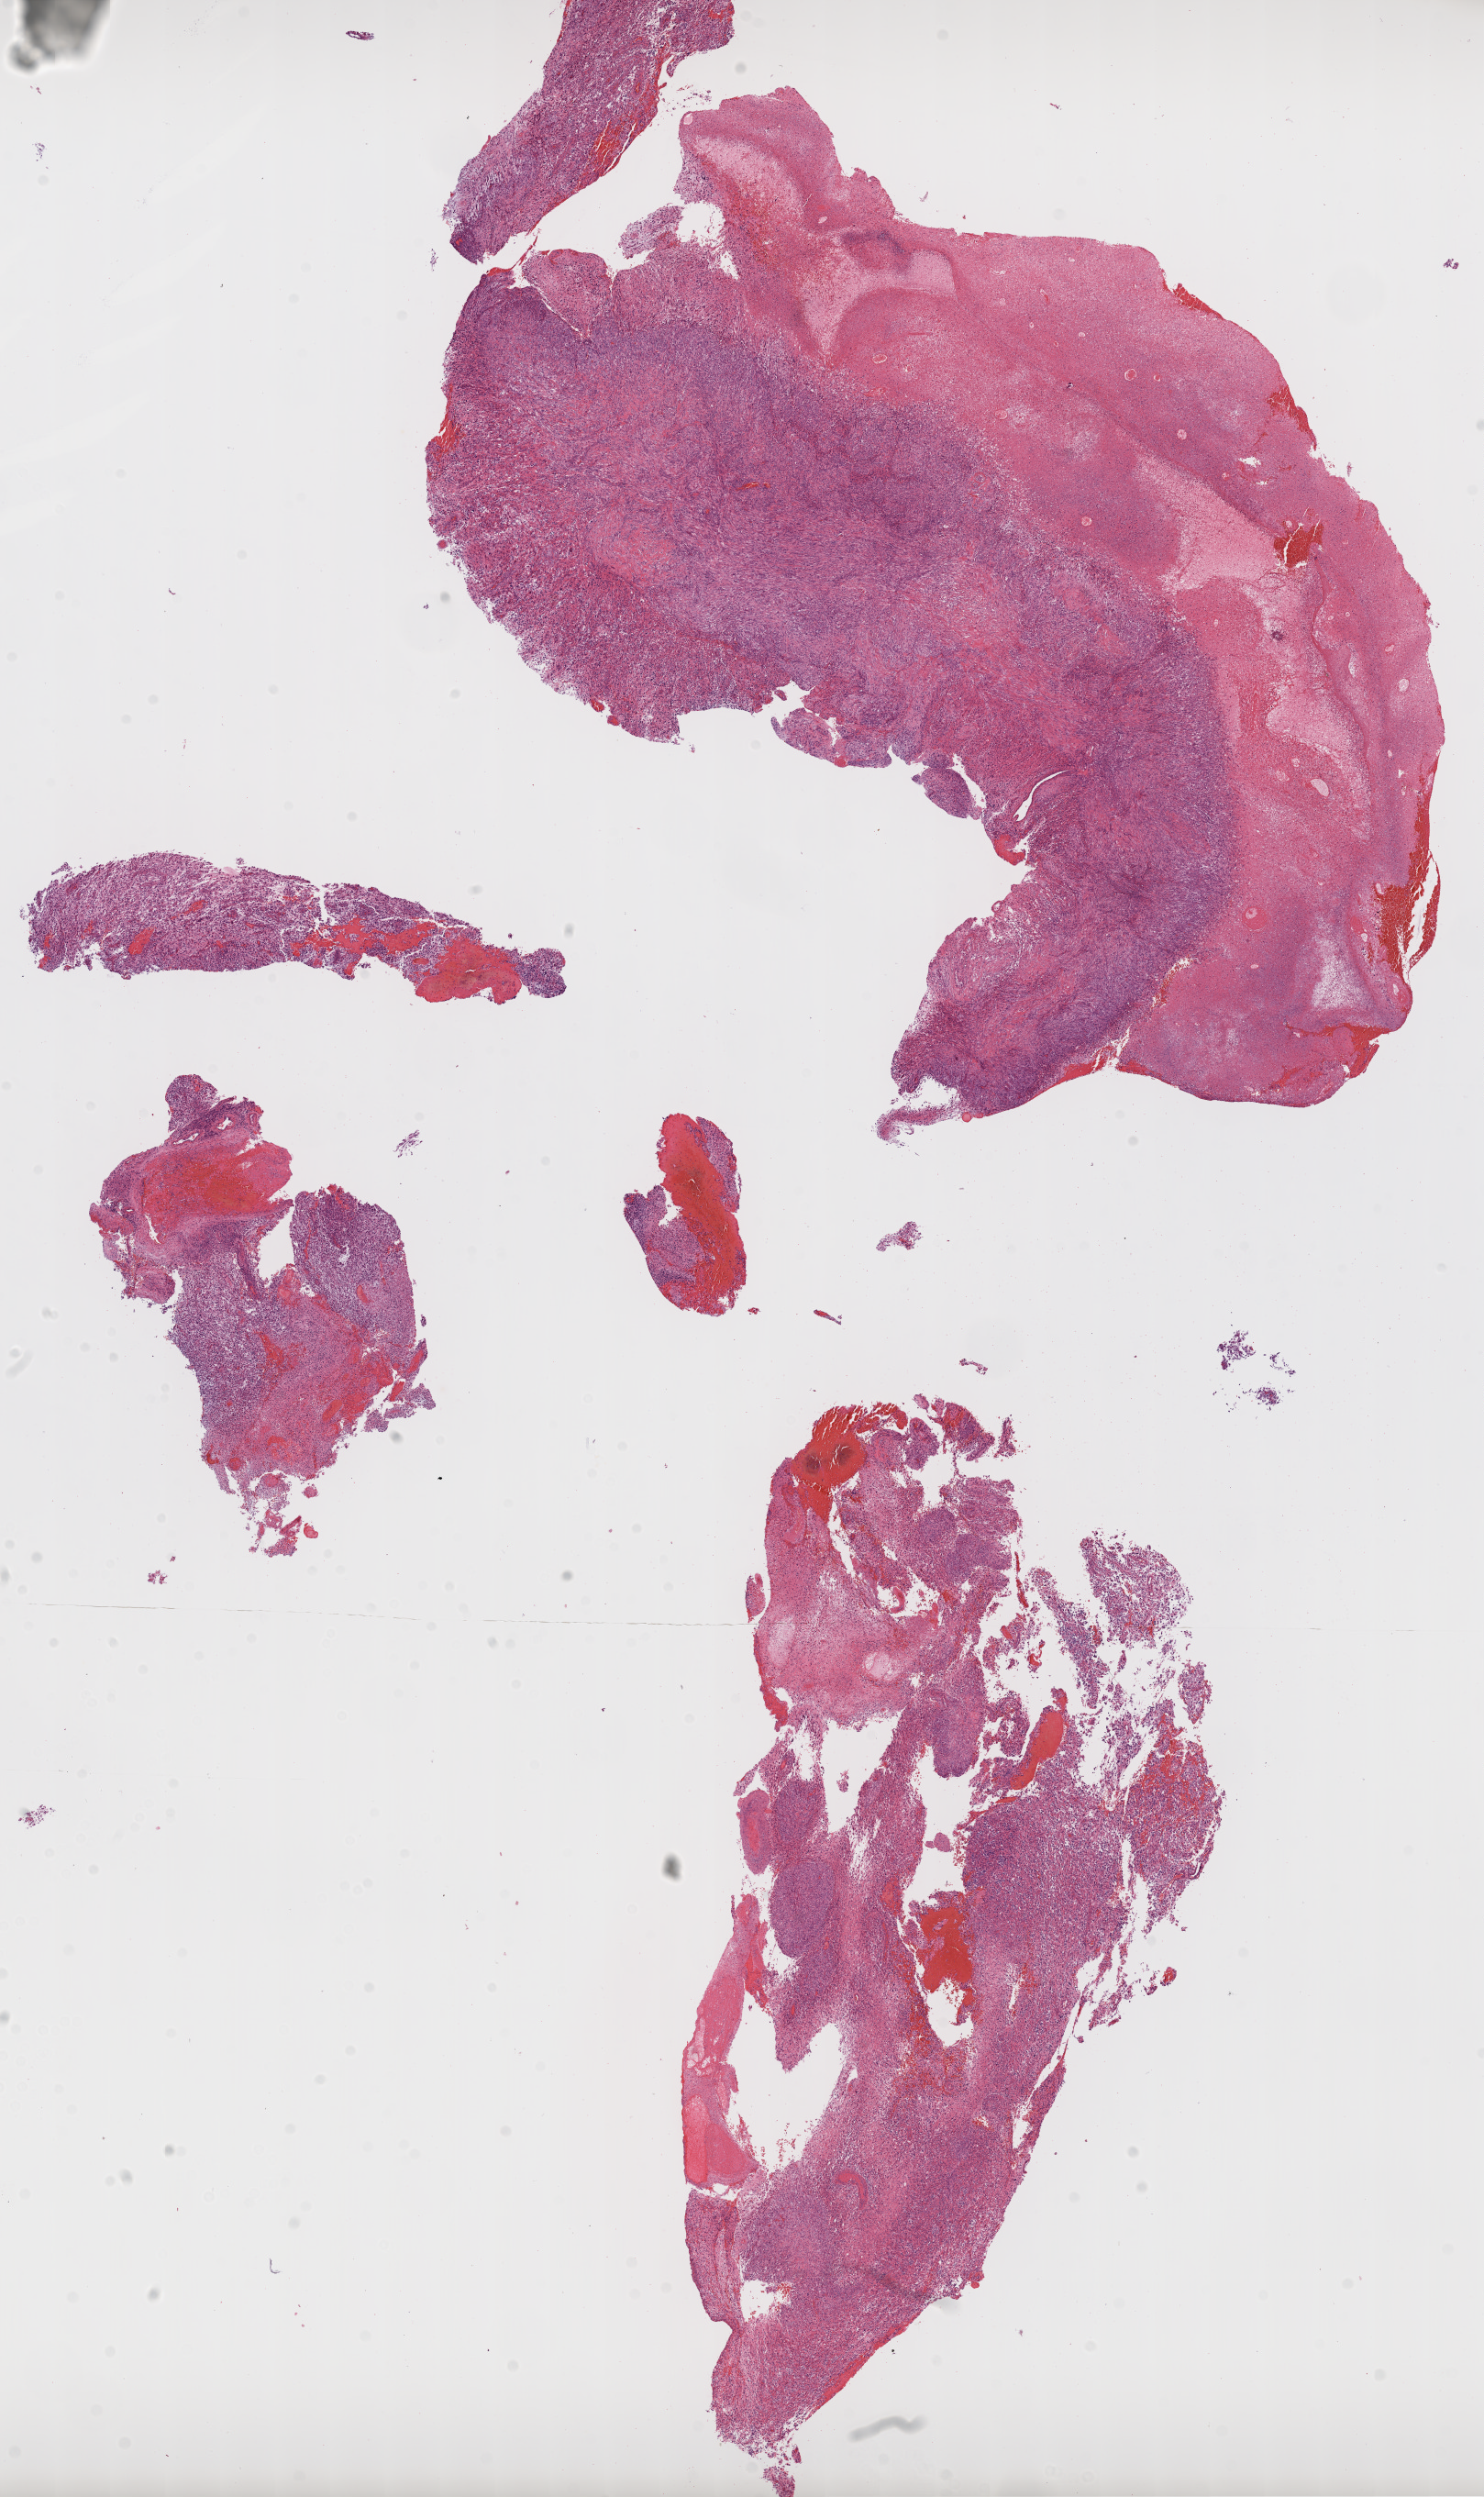
Digitized Hematoxylin and eosin (H&E) stained tissue section (whole slide), low-resolution overview of the scanned area, about 13.1 x 22.0 mm; FFPE section; sample: primary tumour, brain. Patient: male, age at initial diagnosis 57 years.
* diagnosis: Glioblastoma